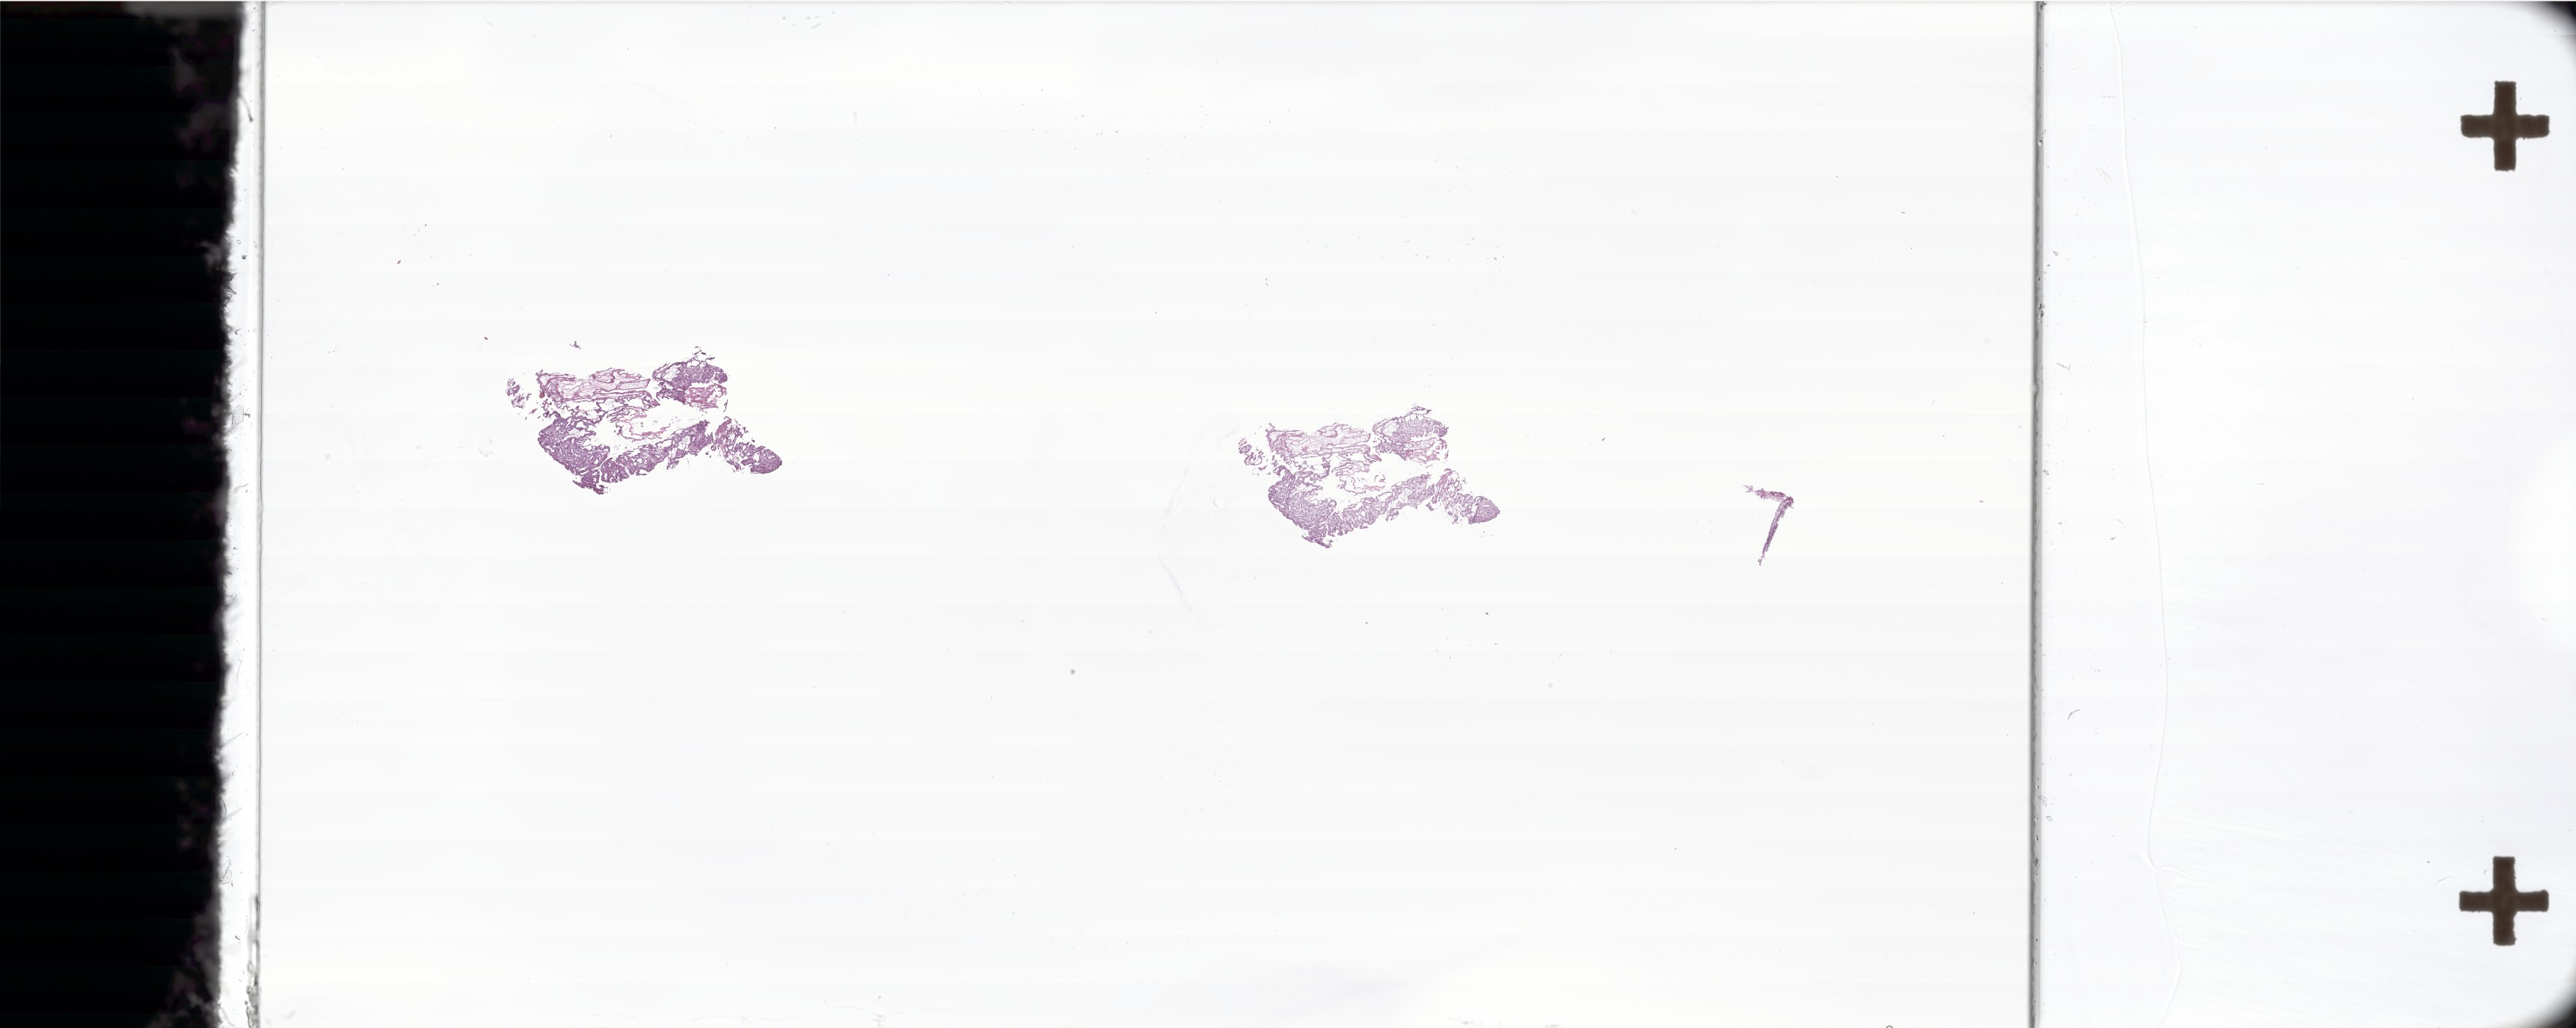
Hematoxylin and eosin (H&E) whole-slide image of tumor tissue from the brain, shown as a low-resolution overview of the whole scanned area (about 58.1 x 23.2 mm). Cryosection (OCT / tissue freezing medium). Patient: male, age 107 months (8 years 11 months).
* recorded diagnosis: Craniopharyngioma, adamantinomatous